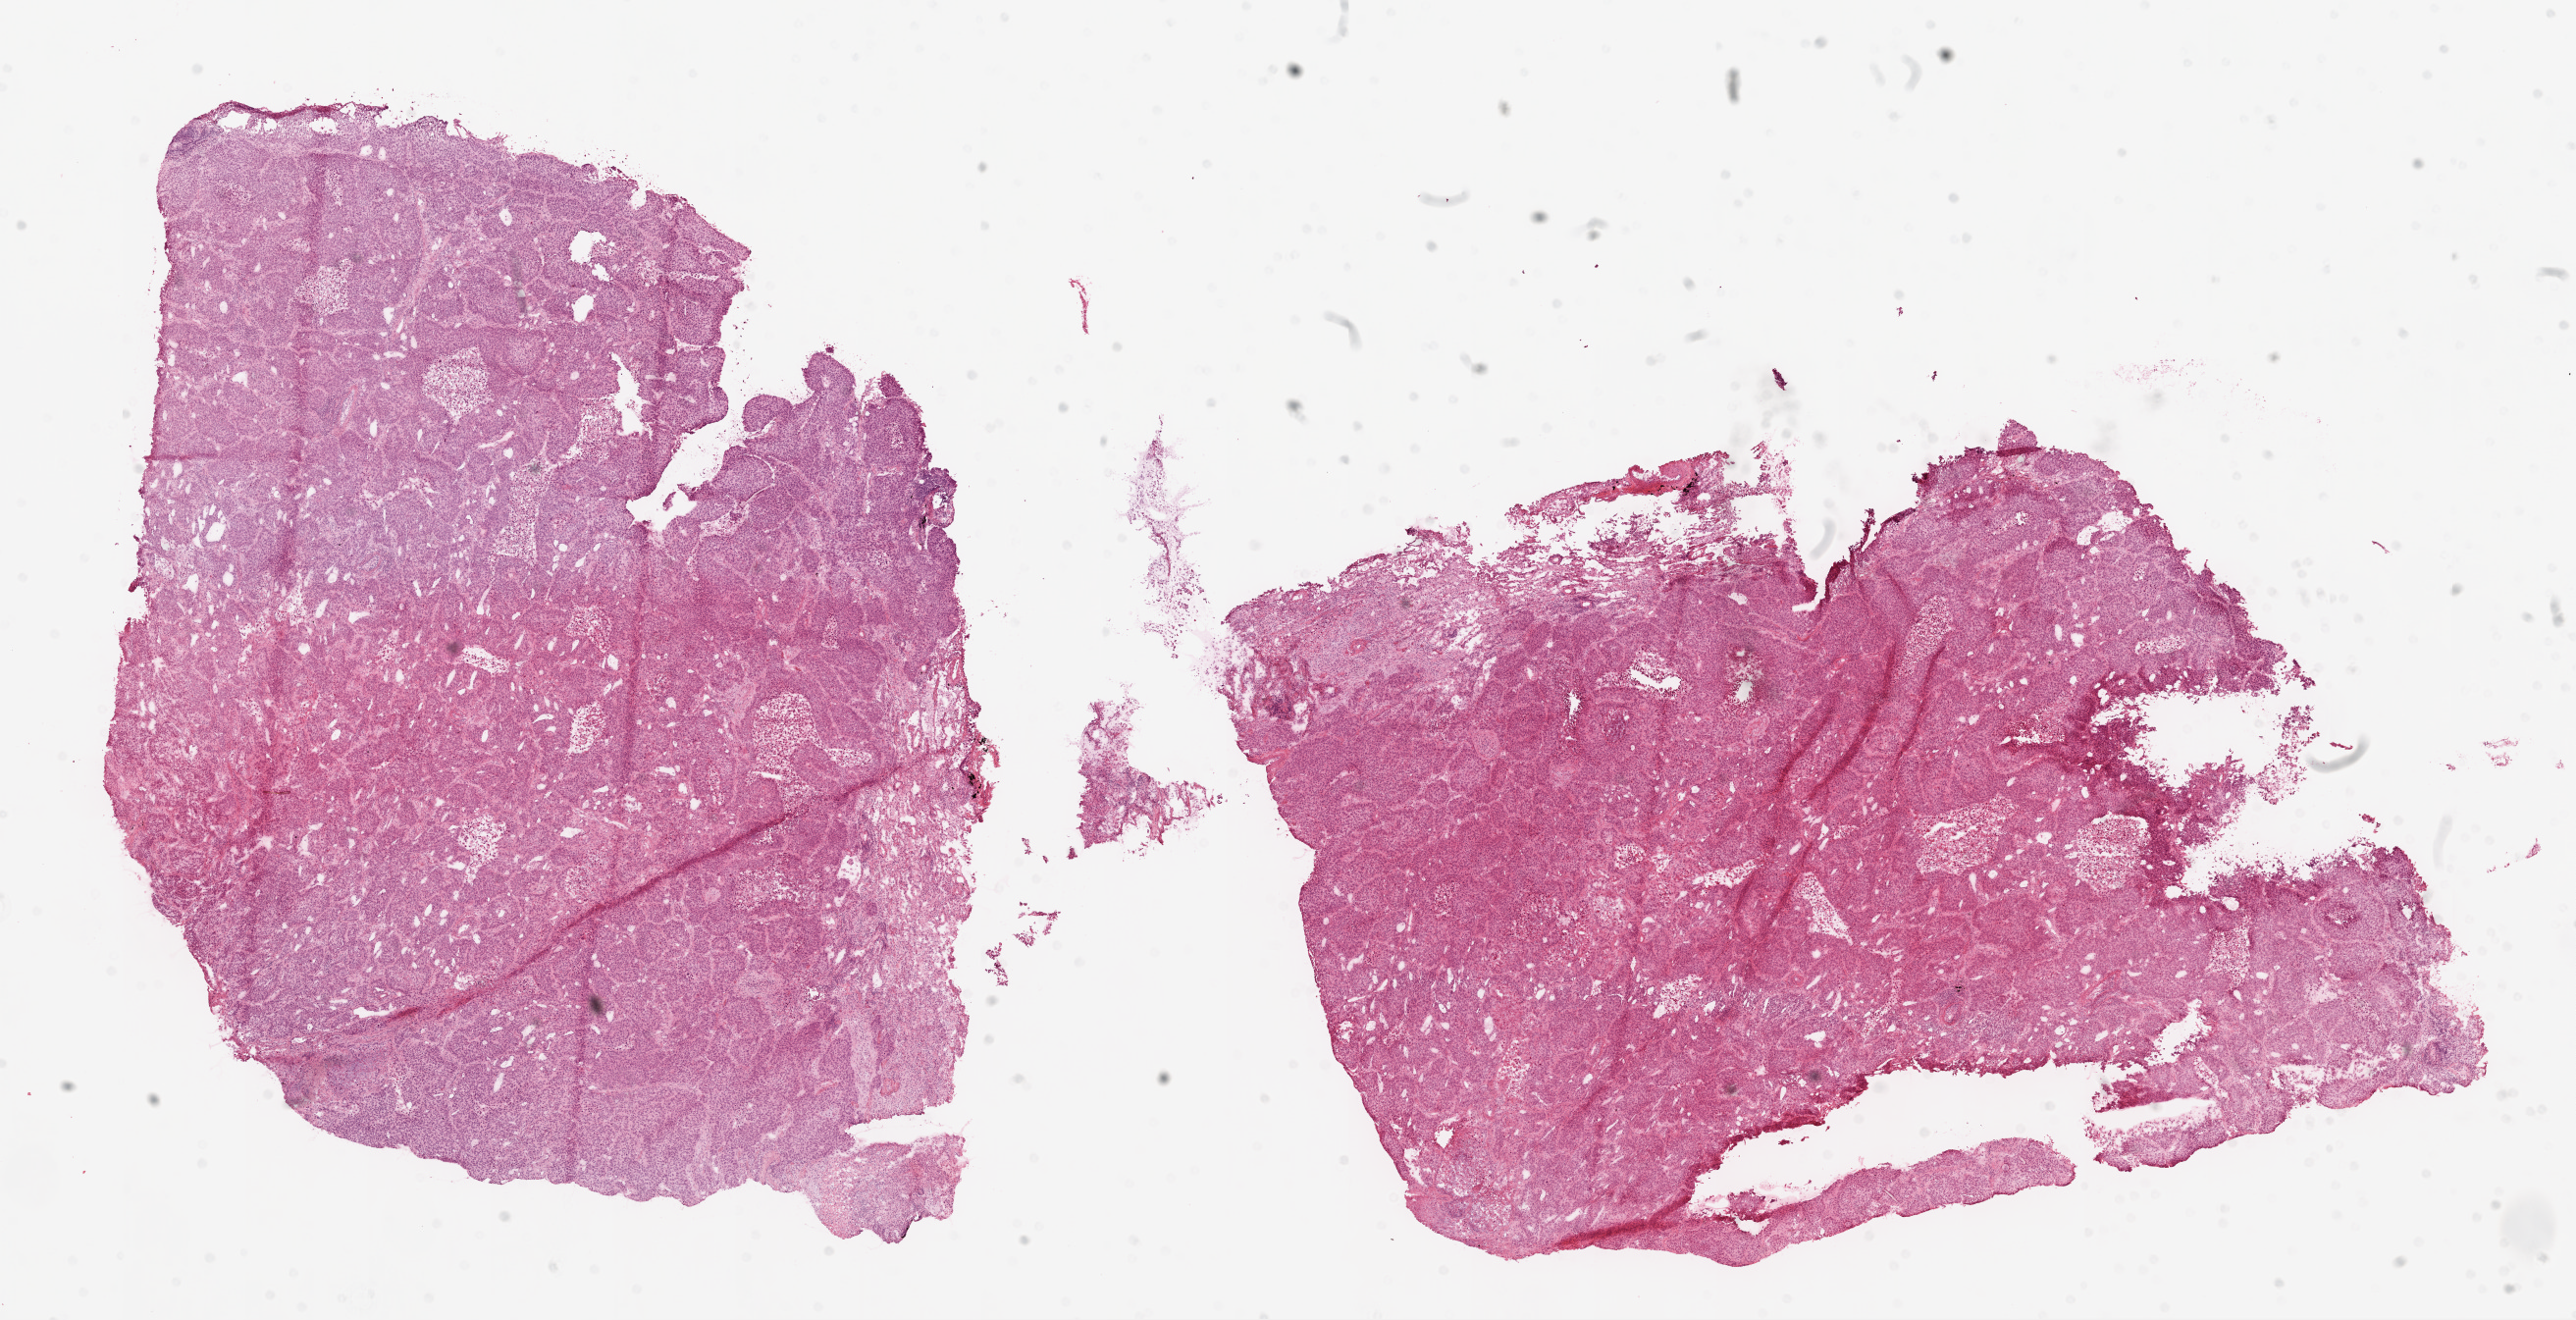
Hematoxylin and eosin (H&E) stained whole-slide image, low-resolution overview of the scanned area, about 21.1 x 10.8 mm (from a 20x scan). Frozen section from the top of the tissue portion. Lung, primary tumour sample. Patient: male, age at initial diagnosis 68 years. Pathologist review of this section (percent, as recorded): tumour cells 80%, tumour nuclei 85%, normal cells 5%, stromal cells 5%, necrosis 10%.
• AJCC pathologic stage: IB (5th edition)
• diagnosis: Squamous cell carcinoma, NOS (lower lobe, lung)